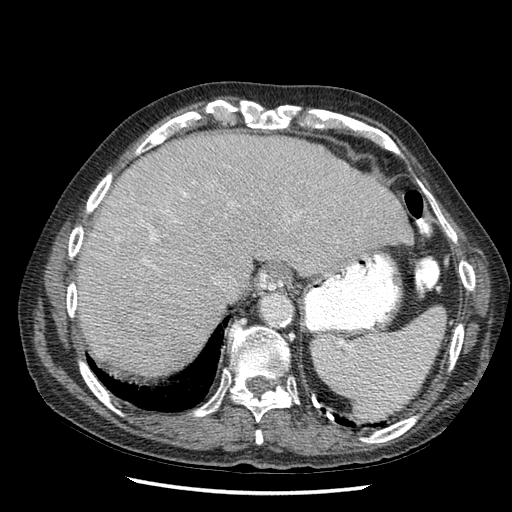
Contrast-enhanced abdominal CT (liver protocol), one axial slice. Slice 44 of 67 in the series (ordered by position). Soft-tissue window (W 400 / L 40 HU). 512 × 512 image matrix, field of view 360 × 360 mm. Case-level facts recorded for this patient, not image findings: diagnosis: hepatocellular carcinoma (patient treated with transarterial chemoembolisation; whether this scan precedes or follows treatment is not stated here); TNM stage (as recorded): Stage-I; Child-Pugh class: A; tumour differentiation: moderately differentiated; tumour nodularity: uninodular.
Structures marked on this image (semi-automatic segmentation, software-assisted and operator-edited):
- liver parenchyma outside the tumour (the mass and vessels are separate outlines, so this box may not span the whole liver): bounding box <78,132,412,380> (left, top, right, bottom; pixels)
- mass: <118,279,164,339>
- liver vessels: <116,202,255,246>